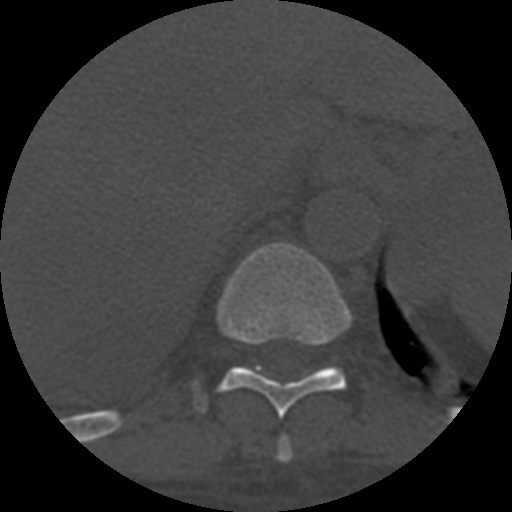
CT including the spine, one axial slice; position 355 of 708 along the scan axis; reconstruction kernel STANDARD; 120 kVp; one of 3 acquisitions stored at this slice position; bone window (W 1800 / L 400 HU); 1.25 mm slice thickness; 512 × 512 image matrix. Patient age 55 years. From the clinical record (not read from this slice): primary cancer: colon; vertebrae with lytic lesions (as recorded): T12, L1, L5.
Structures marked on this image (semi-automatically segmented with operator editing):
- T10 vertebra: bounding box [x1, y1, x2, y2] px = [195, 243, 352, 418]
- T11 vertebra: [317, 370, 324, 373]
- T9 vertebra: [277, 436, 293, 463]